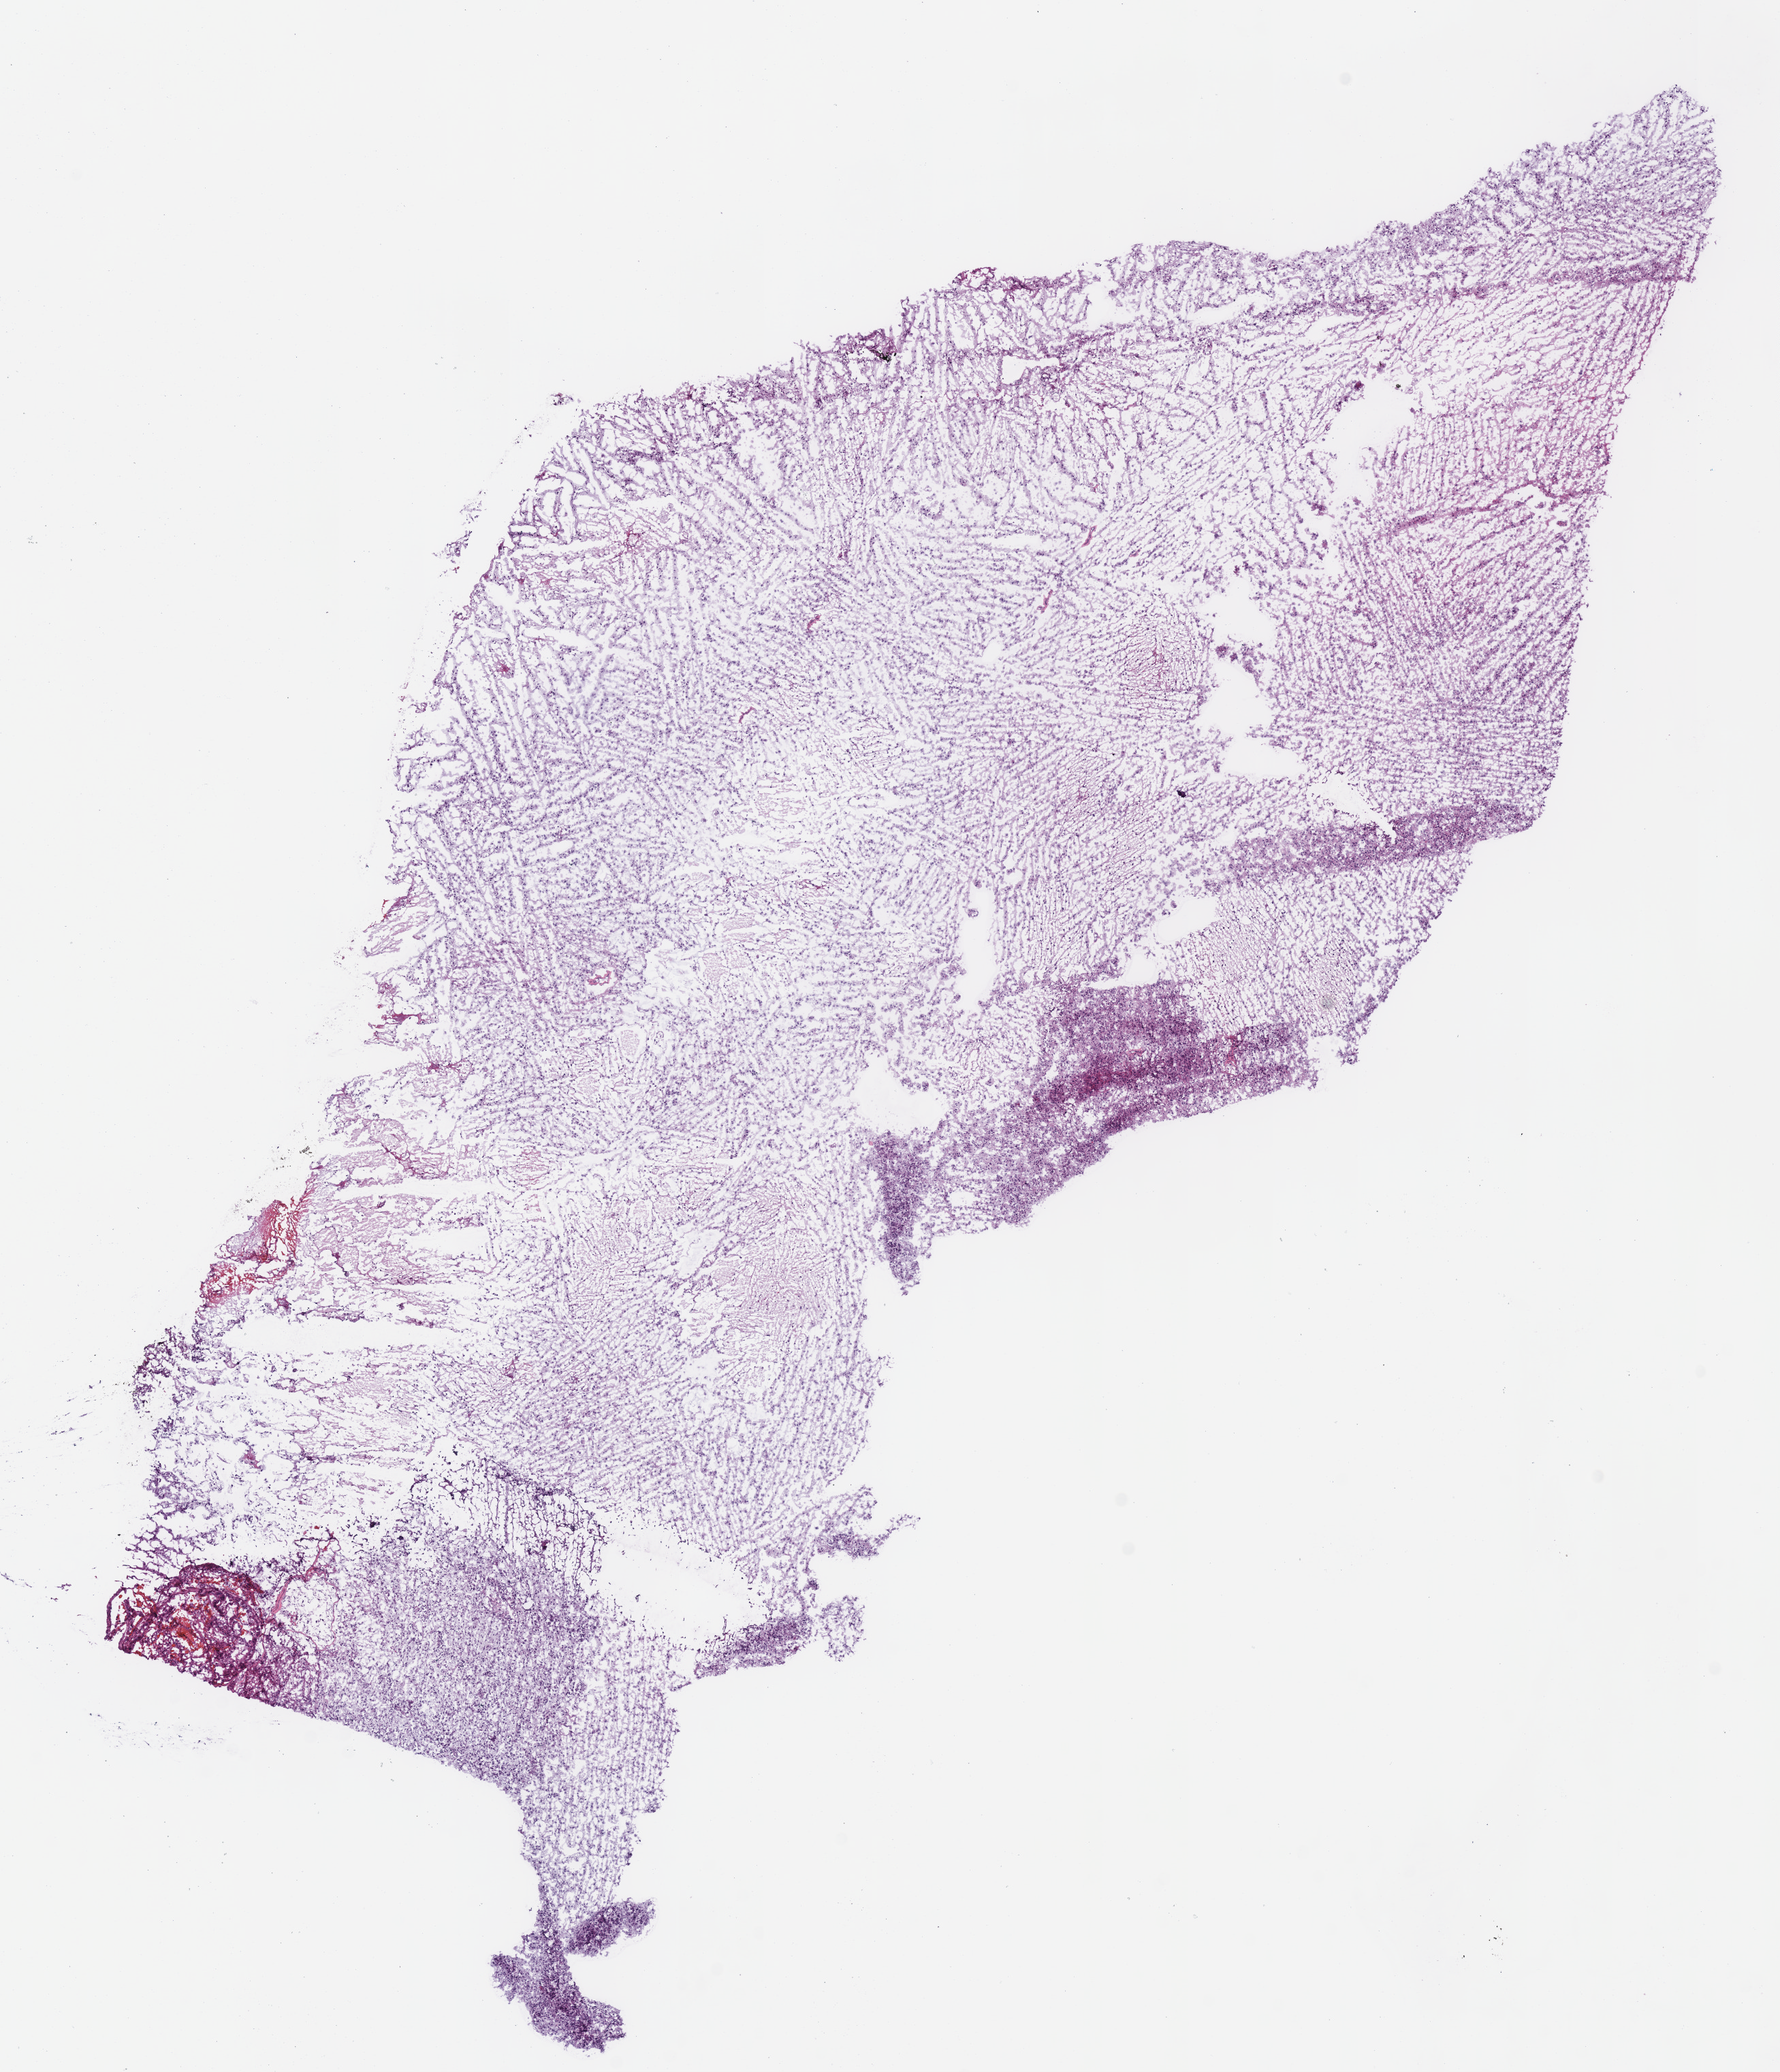
Whole-slide histology image, Hematoxylin and eosin (H&E) stained — whole scanned area (about 10.3 x 12.0 mm, from a 40x scan) shown as a low-resolution overview. Frozen section from the bottom of the tissue portion. Primary tumour sample from the brain. Male, age 36 years at initial diagnosis. Histologic grade: G3 (poorly differentiated). Slide review estimates, as recorded: tumour cells 100%, tumour nuclei 80%, normal cells 0%, stromal cells 0%, necrosis 0%.
Diagnosis: Astrocytoma, anaplastic (cerebrum).